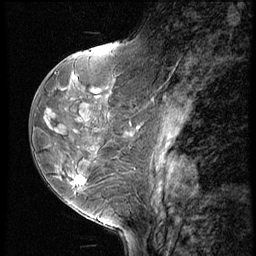
Breast MRI (dynamic contrast-enhanced), one sagittal slice; position 27 of 60 along the scan axis; 3 images stored at this slice position (order not interpretable as contrast timing); 1.5 T; TE 4.2 ms, TR 8.9 ms; 2.5 mm slice thickness; 256 × 256 image matrix, field of view 200 × 200 mm. Patient: female, 50 years. From the clinical record (not read from this slice): setting: breast cancer imaged before/during neoadjuvant chemotherapy; receptor status: HR-positive, HER2-negative.
Annotated regions visible in this slice (semi-automatically segmented with operator editing):
- analysis volume of interest (the breast-tissue region the enhancement analysis was run in; not a lesion): bounding box (x1, y1, x2, y2) in pixels: (38, 102, 118, 213)
- tumour enhancement mask (voxels above the 140 % enhancement threshold inside the analysis volume of interest): (72, 176, 87, 185)